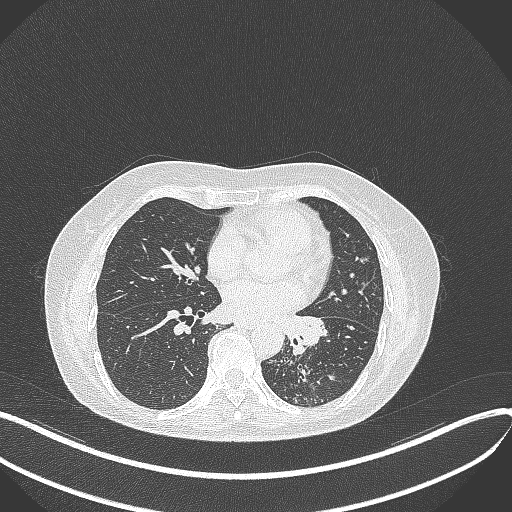
Chest CT, one axial slice. Slice 186 of 429 in the series (ordered by position). Lung window (W 1500 / L -600 HU). 512 × 512 image matrix. Patient: female, 63 years. Case-level facts recorded for this patient, not image findings: clinical TNM (as recorded): T1b N0 M0; histopathological grade: G2-3.
Annotated regions visible in this slice (rectangle marked by the reading radiologist):
- lung tumour (recorded histology: adenocarcinoma): bounding box <283,311,329,357> (left, top, right, bottom; pixels)